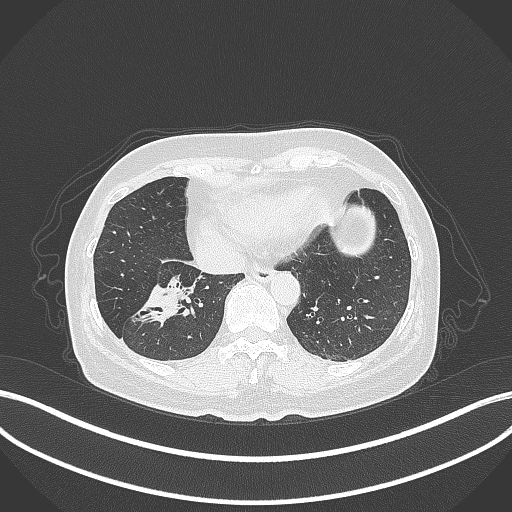
Chest CT, one axial slice; slice 114 of 429 in the series (ordered by position); reconstruction kernel B70f; lung window (W 1500 / L -600 HU); 1 mm slice thickness; 512 × 512 image matrix. Female patient, age 67 years. Case-level facts recorded for this patient, not image findings: clinical TNM (as recorded): T1c N1 M0; histopathological grade: G2-3.
Annotated regions visible in this slice (rectangle marked by the reading radiologist):
- lung tumour (recorded histology: adenocarcinoma): bounding box (x1, y1, x2, y2) in pixels: (134, 276, 195, 329)